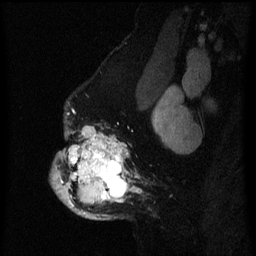
Breast MRI (dynamic contrast-enhanced), one sagittal slice. Position 47 of 60 along the scan axis. Dynamic contrast-enhanced series, image 2 of 3 at this slice position (ordered by acquisition). 1.5 T. TE 4.2 ms, TR 8 ms. 2 mm slice thickness. 256 × 256 image matrix, field of view 190 × 190 mm. Patient: female, 50 years.
Annotated regions visible in this slice (semi-automatically segmented with operator editing):
- analysis volume of interest (the breast-tissue region the enhancement analysis was run in; not a lesion): box from (x=50, y=124) to (x=141, y=220) px
- tumour enhancement mask (voxels above the 70 % enhancement threshold inside the analysis volume of interest): (x=52, y=126)–(x=141, y=218)